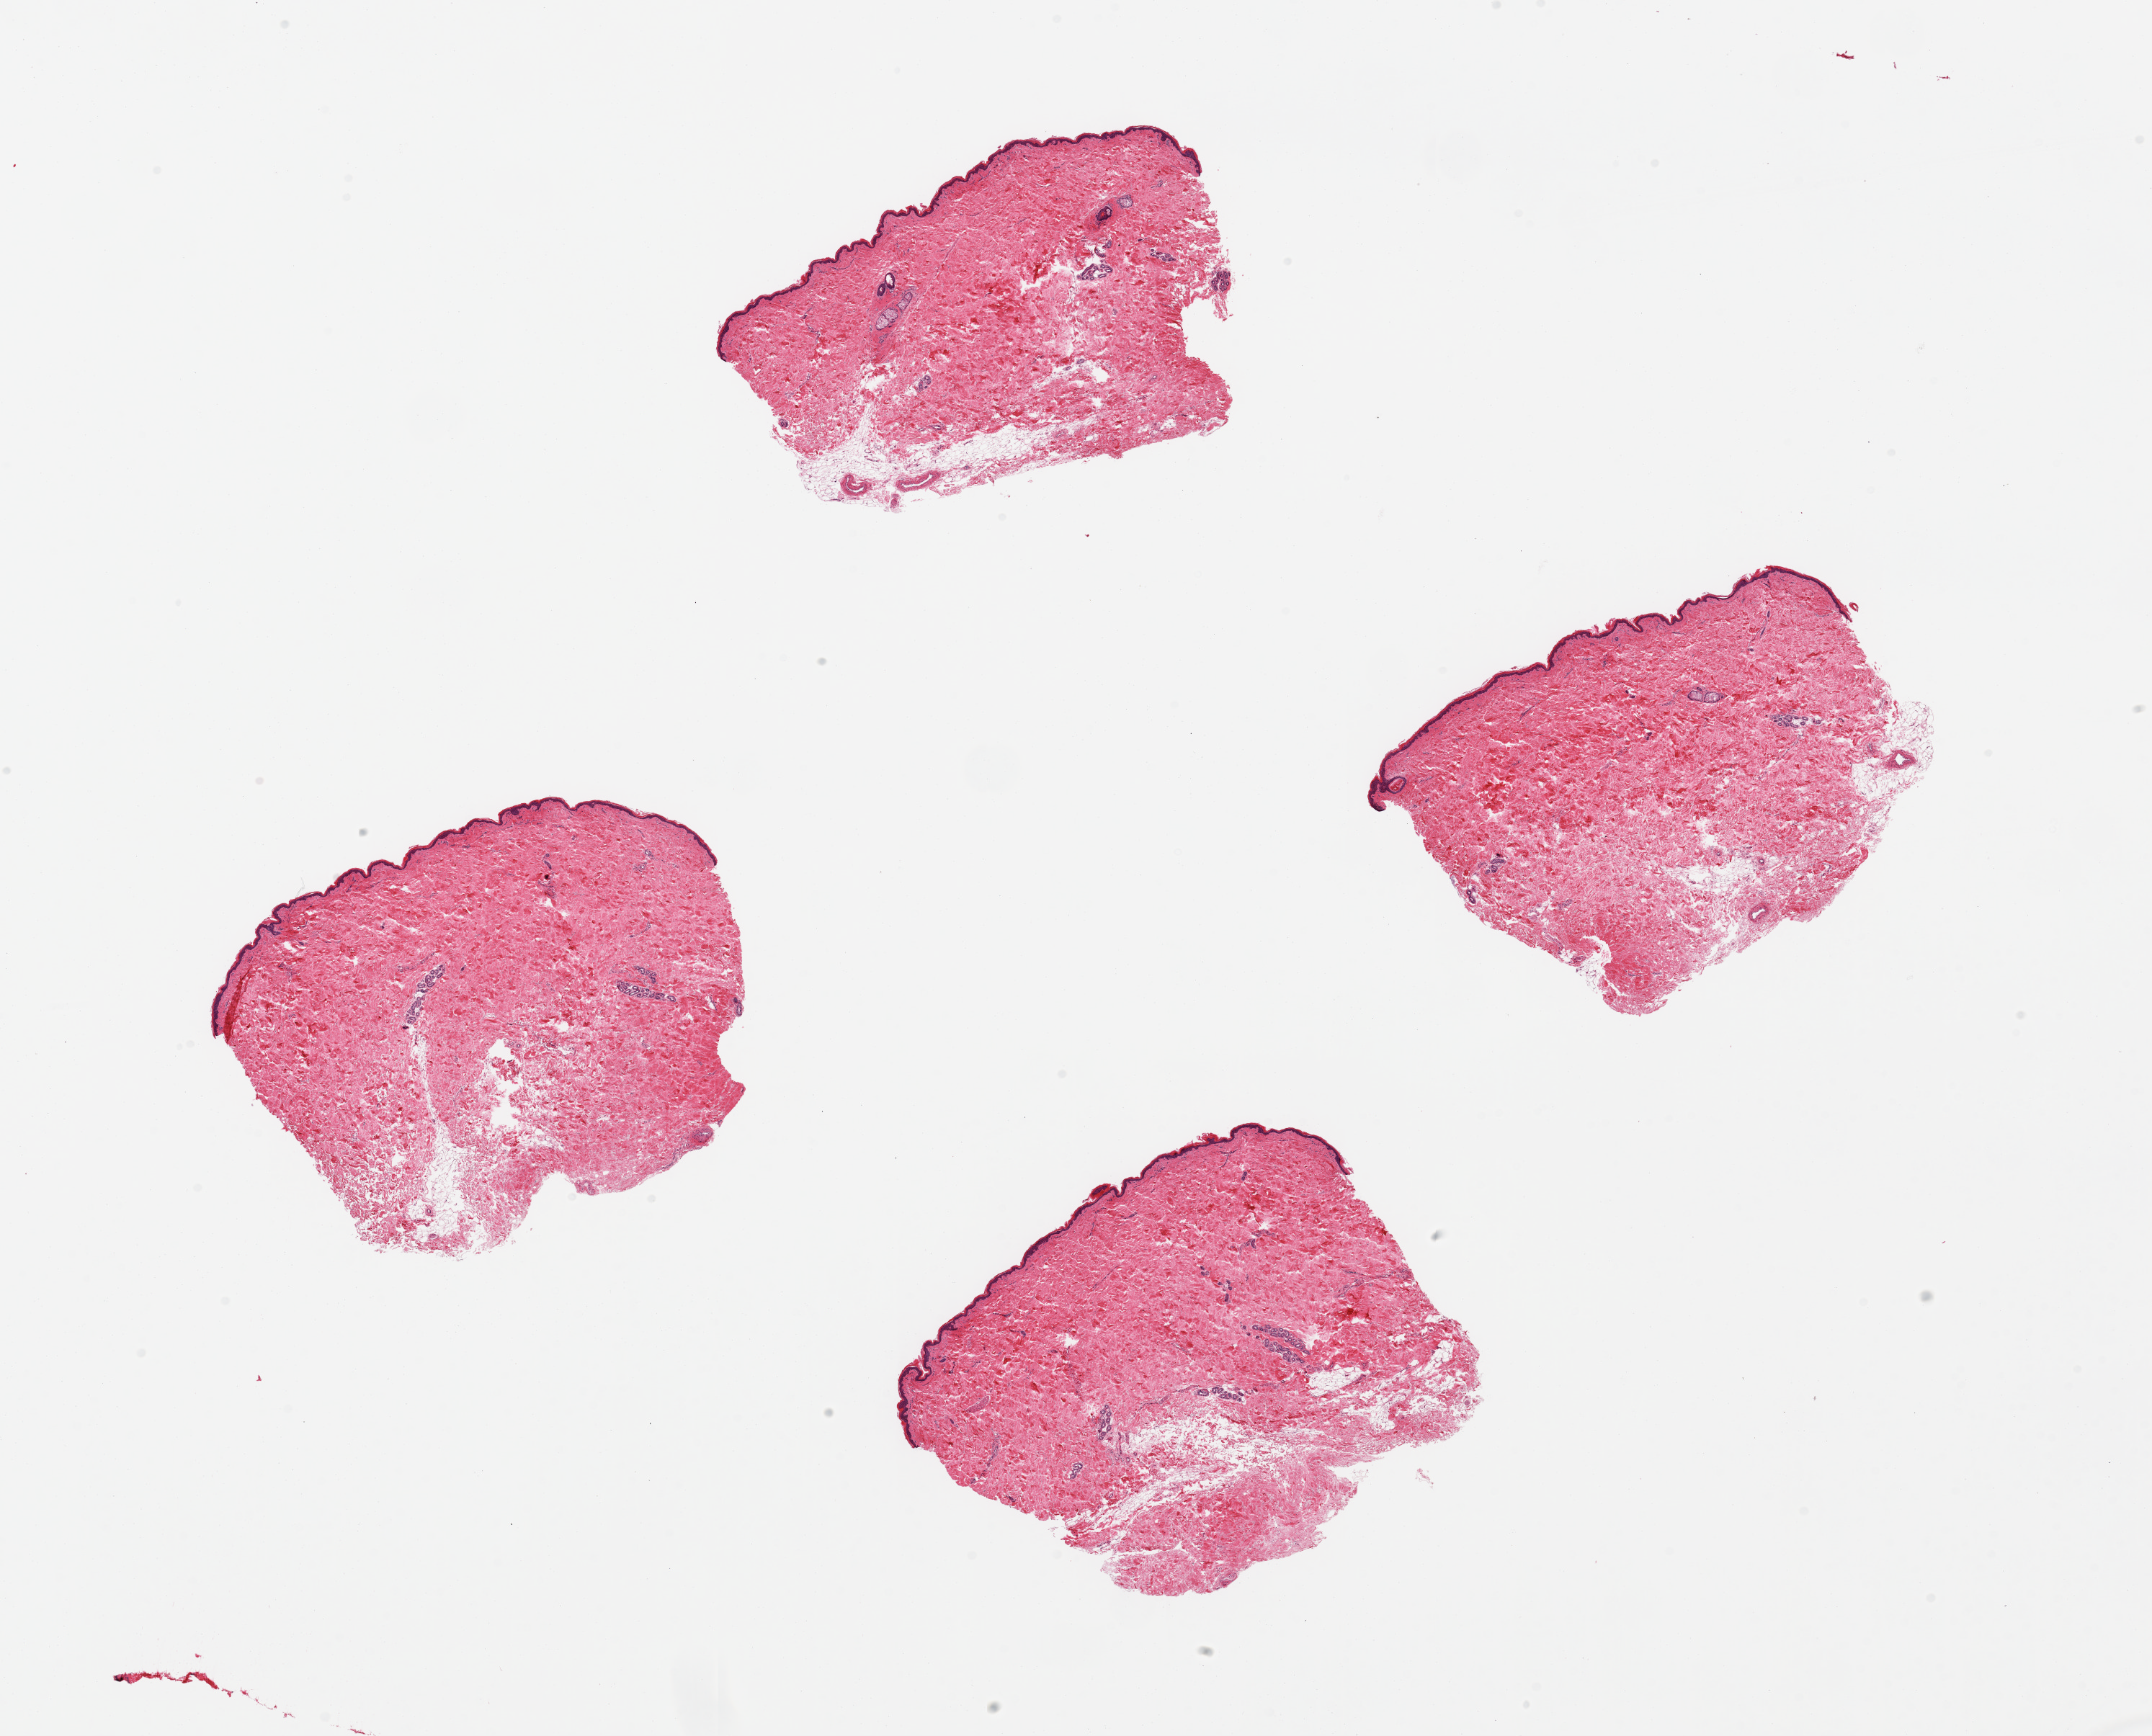
Whole-slide image, H&E stain, low-resolution overview of the scanned area, about 23.6 x 19.1 mm. PAXgene-fixed paraffin-embedded (PFPE) section. Target tissue: skin of suprapubic region. Donor tissue sample.
• reviewer comment on this tissue sample: 4 pieces; includes from 5-10% internal and attached fat